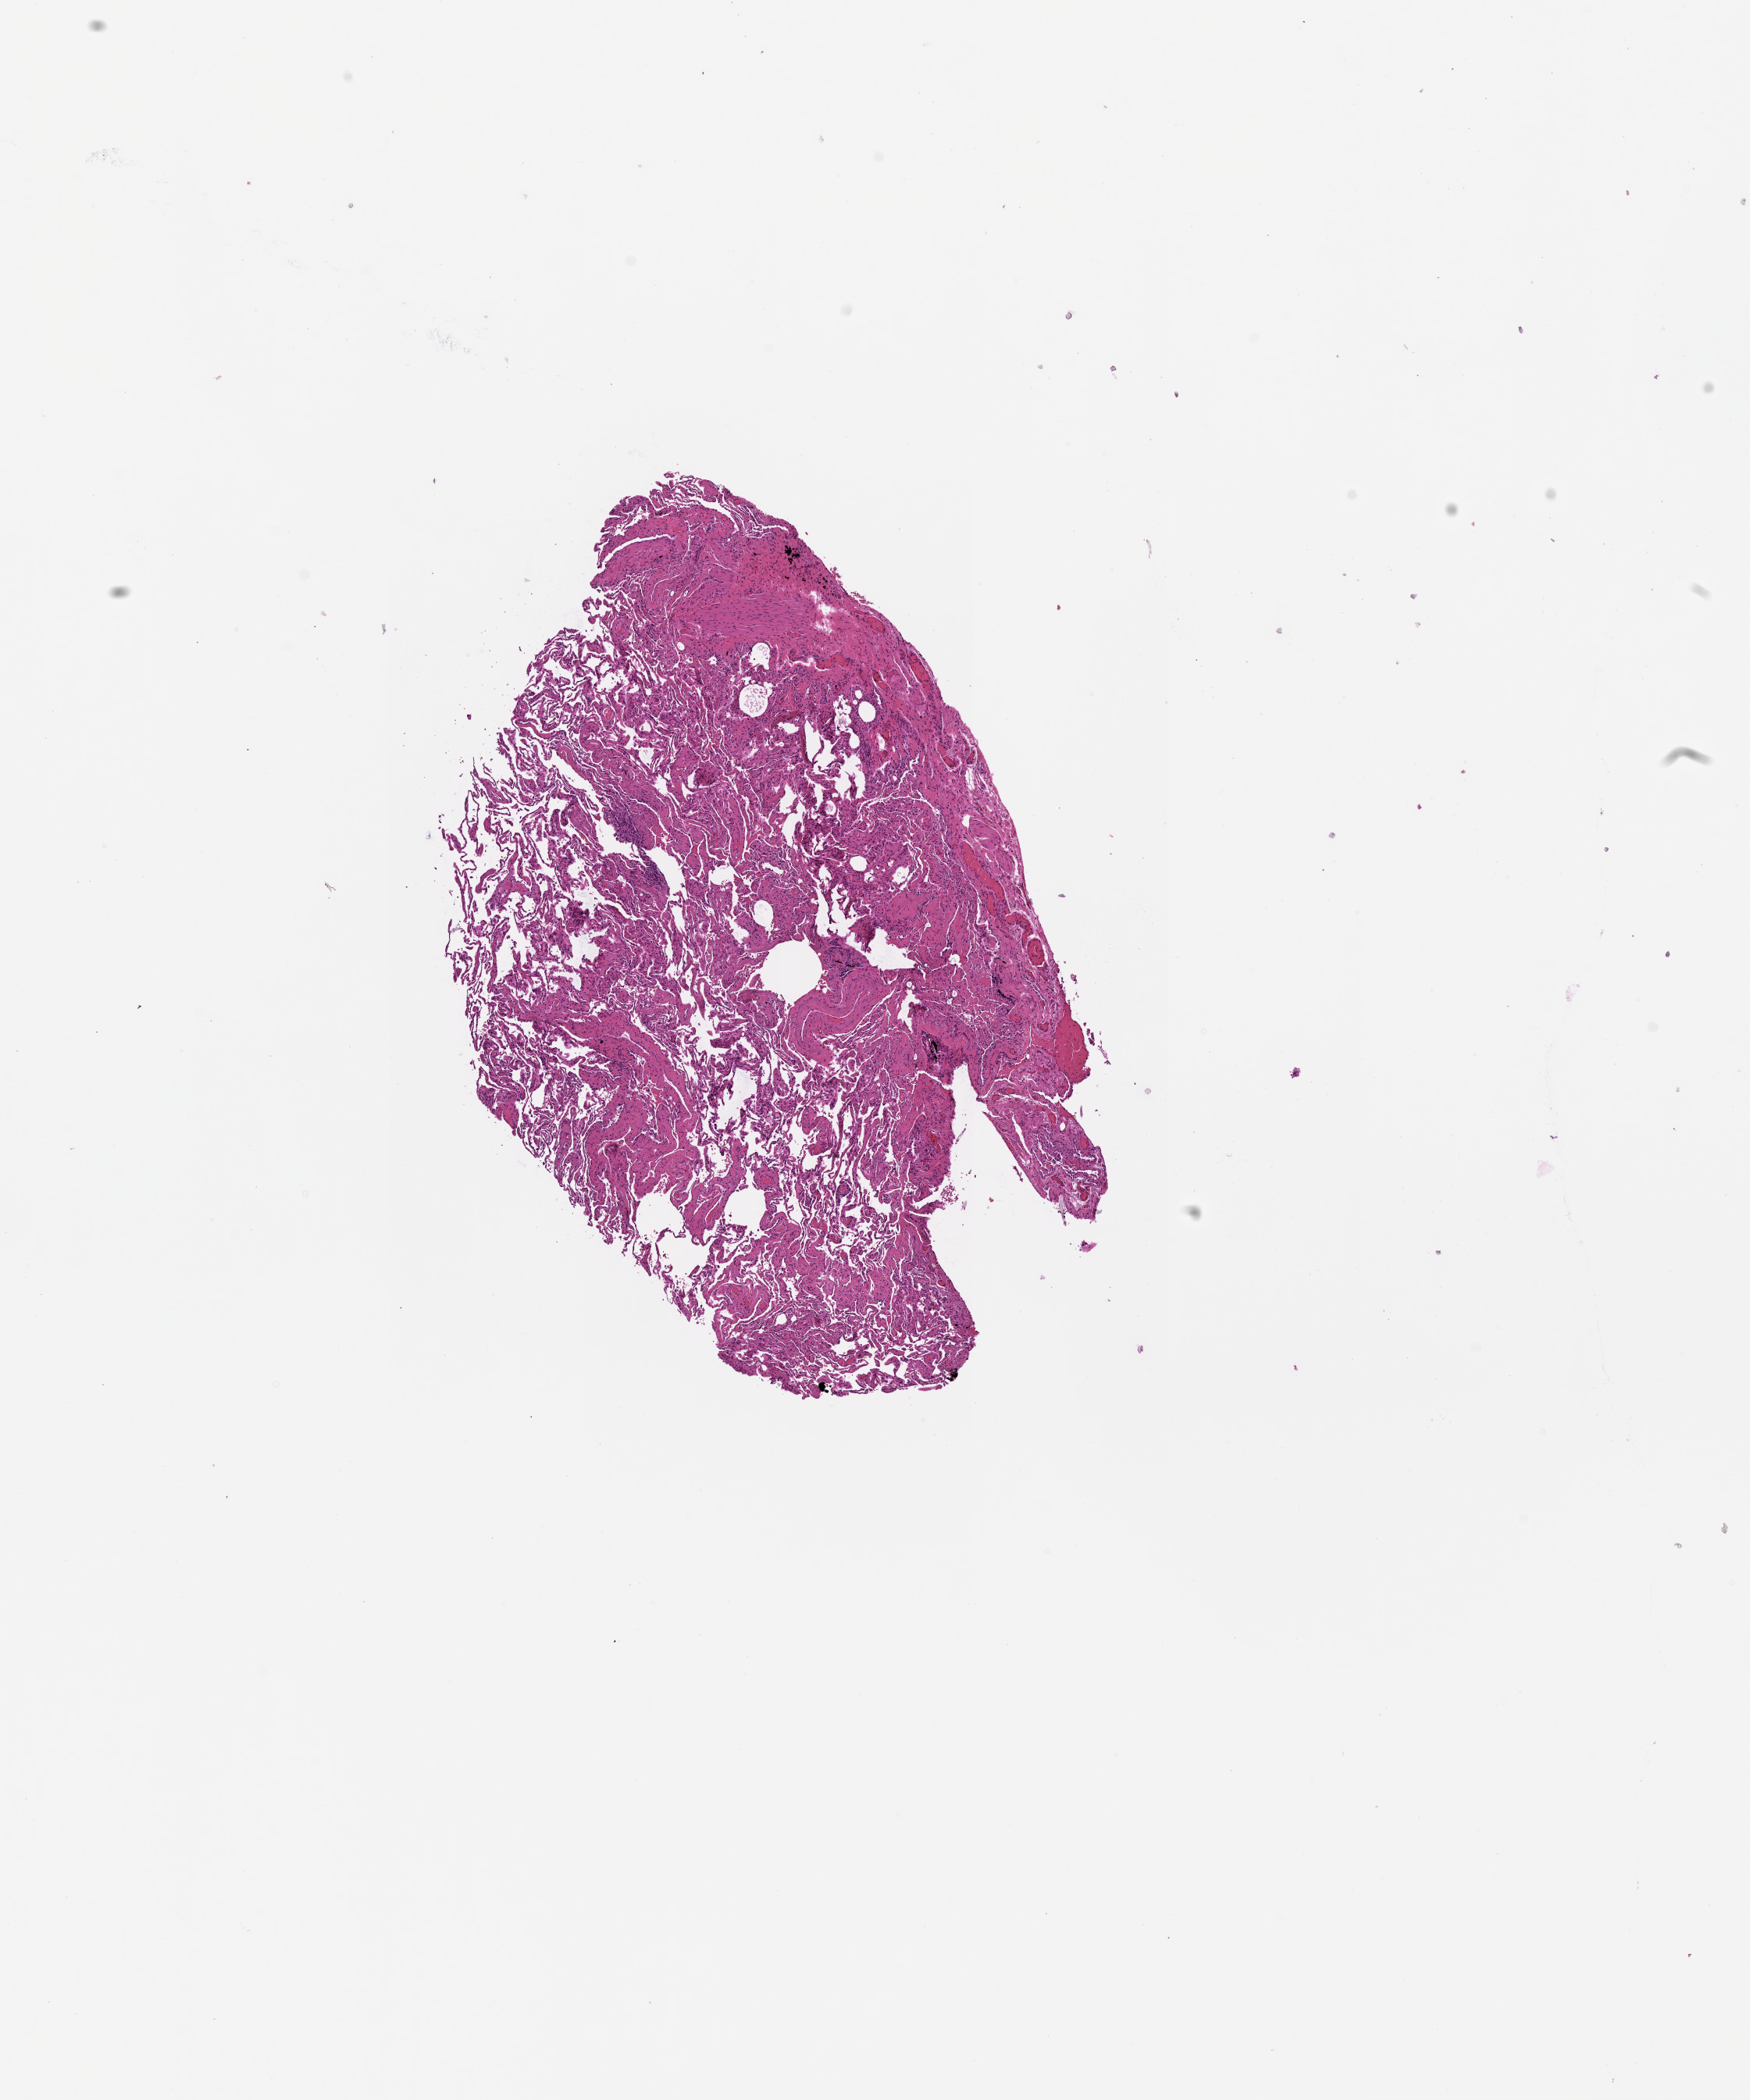
Digitized Hematoxylin and eosin (H&E) stained tissue section (whole slide), whole scanned area (about 9.0 x 10.8 mm) shown as a low-resolution overview. Lung, tissue type not recorded.
• patient diagnosis (cohort enrolment): squamous cell carcinoma (lung)